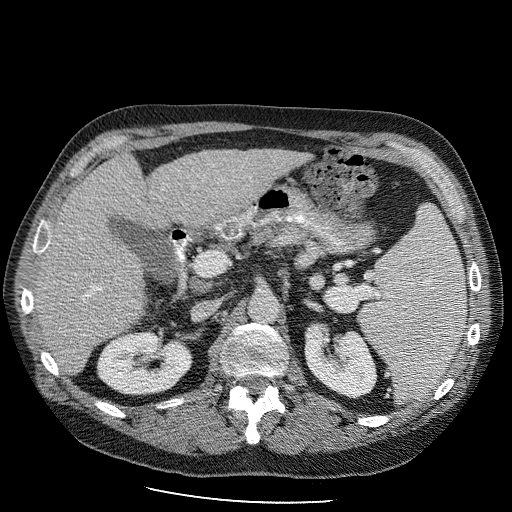
Contrast-enhanced abdominal CT (liver protocol), one axial slice; reconstruction kernel STANDARD; 120 kVp; soft-tissue window (W 400 / L 40 HU); 2.5 mm slice thickness; 512 × 512 image matrix, field of view 400 × 400 mm. From the clinical record (not read from this slice): diagnosis: hepatocellular carcinoma (patient treated with transarterial chemoembolisation; whether this scan precedes or follows treatment is not stated here); TNM stage (as recorded): Stage-II; Child-Pugh class: B.
Outlined on this slice (semi-automatic segmentation, software-assisted and operator-edited):
- liver parenchyma outside the tumour (the mass and vessels are separate outlines, so this box may not span the whole liver): box from (x=35, y=148) to (x=310, y=374) px
- liver vessels: (x=79, y=227)–(x=84, y=297)